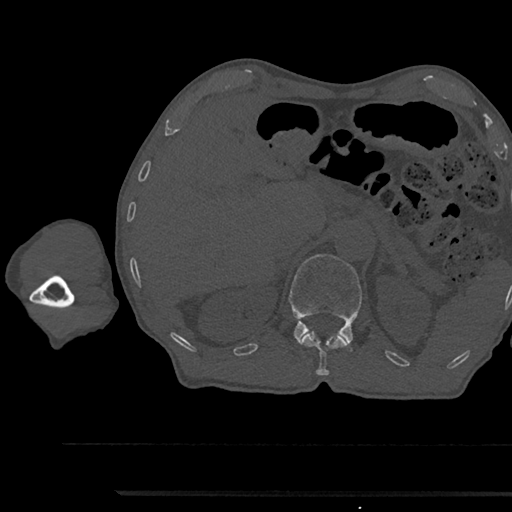
CT including the spine, one axial slice. Position 674 of 797 along the scan axis. Reconstruction kernel Br40s/3. Bone window (W 1800 / L 400 HU). 0.5 mm slice thickness. 512 × 512 image matrix, field of view 367 × 367 mm. Male patient, age 79 years. From the clinical record (not read from this slice): primary cancer: prostate.
Structures marked on this image (semi-automatic segmentation, software-assisted and operator-edited):
- L1 vertebra: bounding box <289,254,362,352> (left, top, right, bottom; pixels)
- T12 vertebra: <299,331,350,375>